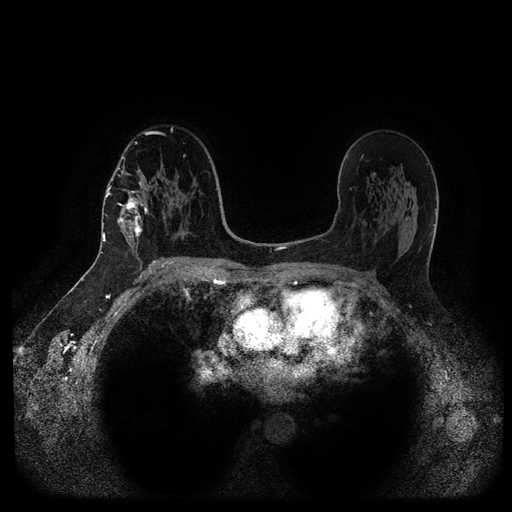
Breast MRI (dynamic contrast-enhanced, multi-phase), one axial slice; position 61 of 116 along the scan axis; dynamic contrast-enhanced series, time point 2 of 5 at this slice position (early post-contrast); 1.5 T; TE 2.6 ms, TR 5.3 ms; 2 mm slice thickness; 512 × 512 image matrix, field of view 360 × 360 mm. Female patient, age 58 years.
Annotated regions visible in this slice (semi-automatically segmented with operator editing):
- breast lesion (labelled 'tumour' in the annotation; benign lesions carry a separate 'benign' label): bounding box <114,196,150,241> (left, top, right, bottom; pixels)